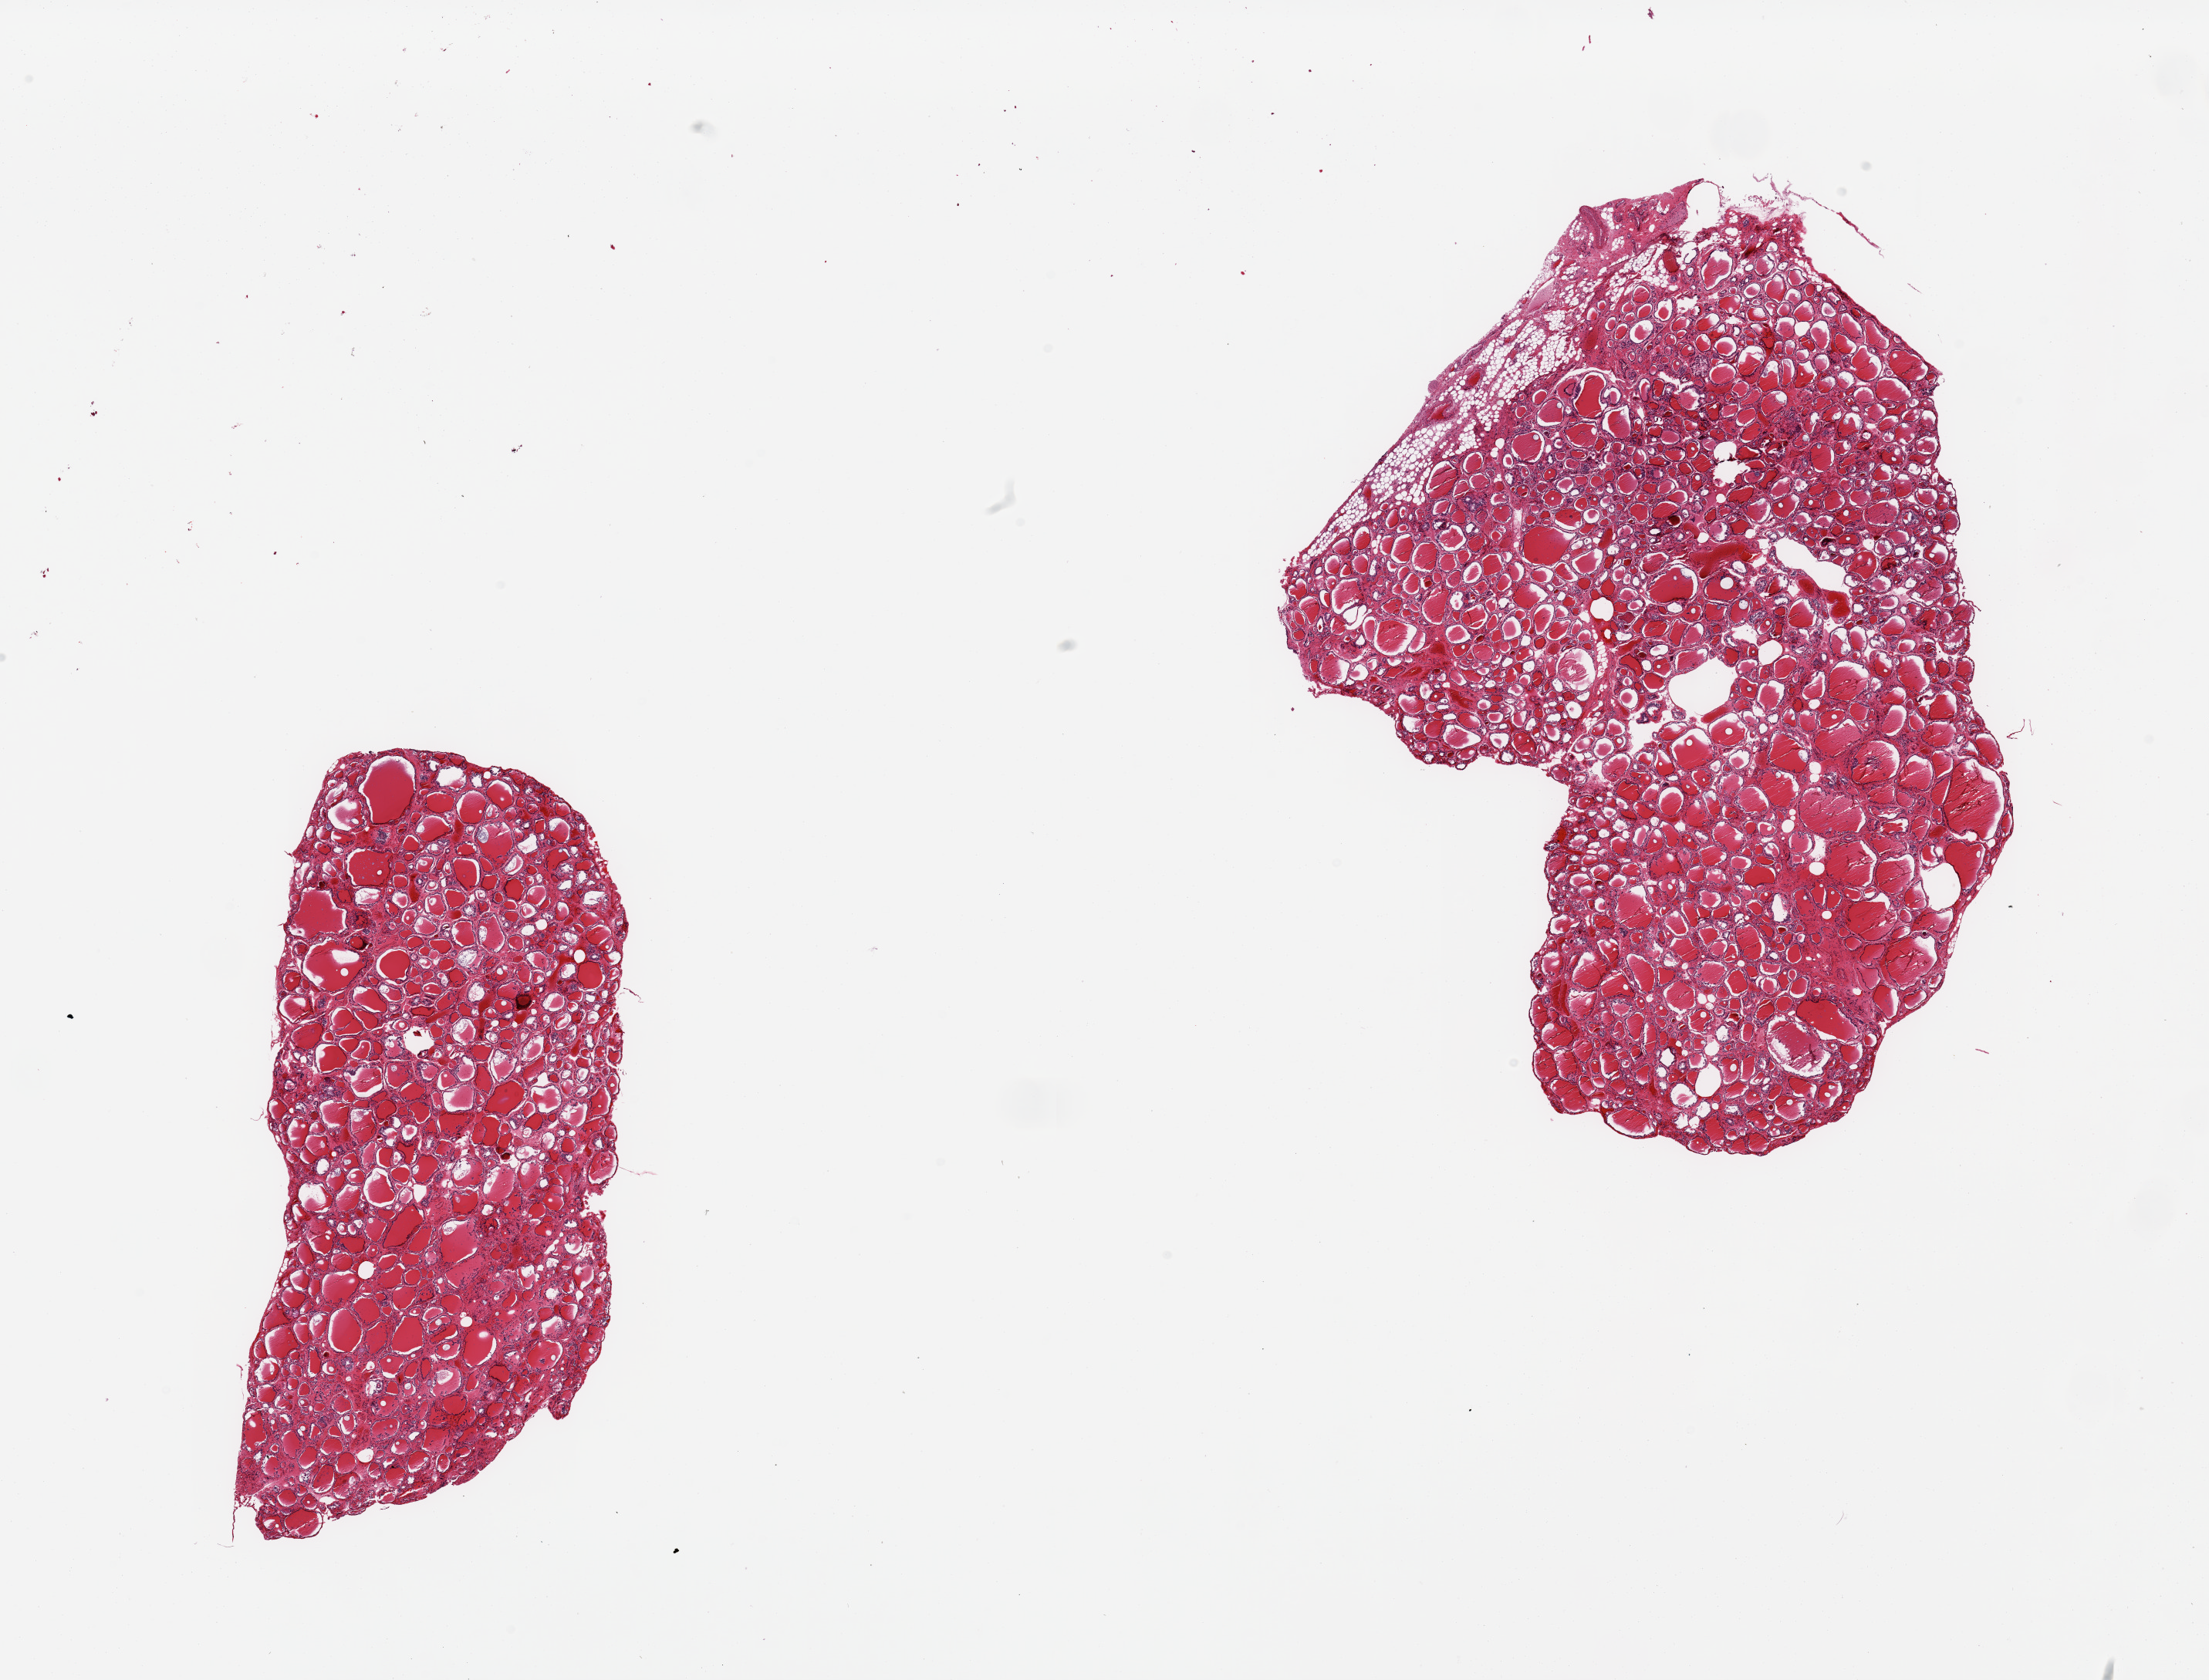
Hematoxylin and eosin (H&E) whole-slide image — shown as a low-resolution overview of the whole scanned area (about 22.6 x 17.2 mm, slide scanned at 20x), PAXgene-fixed, paraffin-embedded tissue, sampled site (target tissue): thyroid, donor tissue sample. Male donor.
Reviewer comment on this tissue sample: 2 pieces; 5% fat at edge of 1 piece.